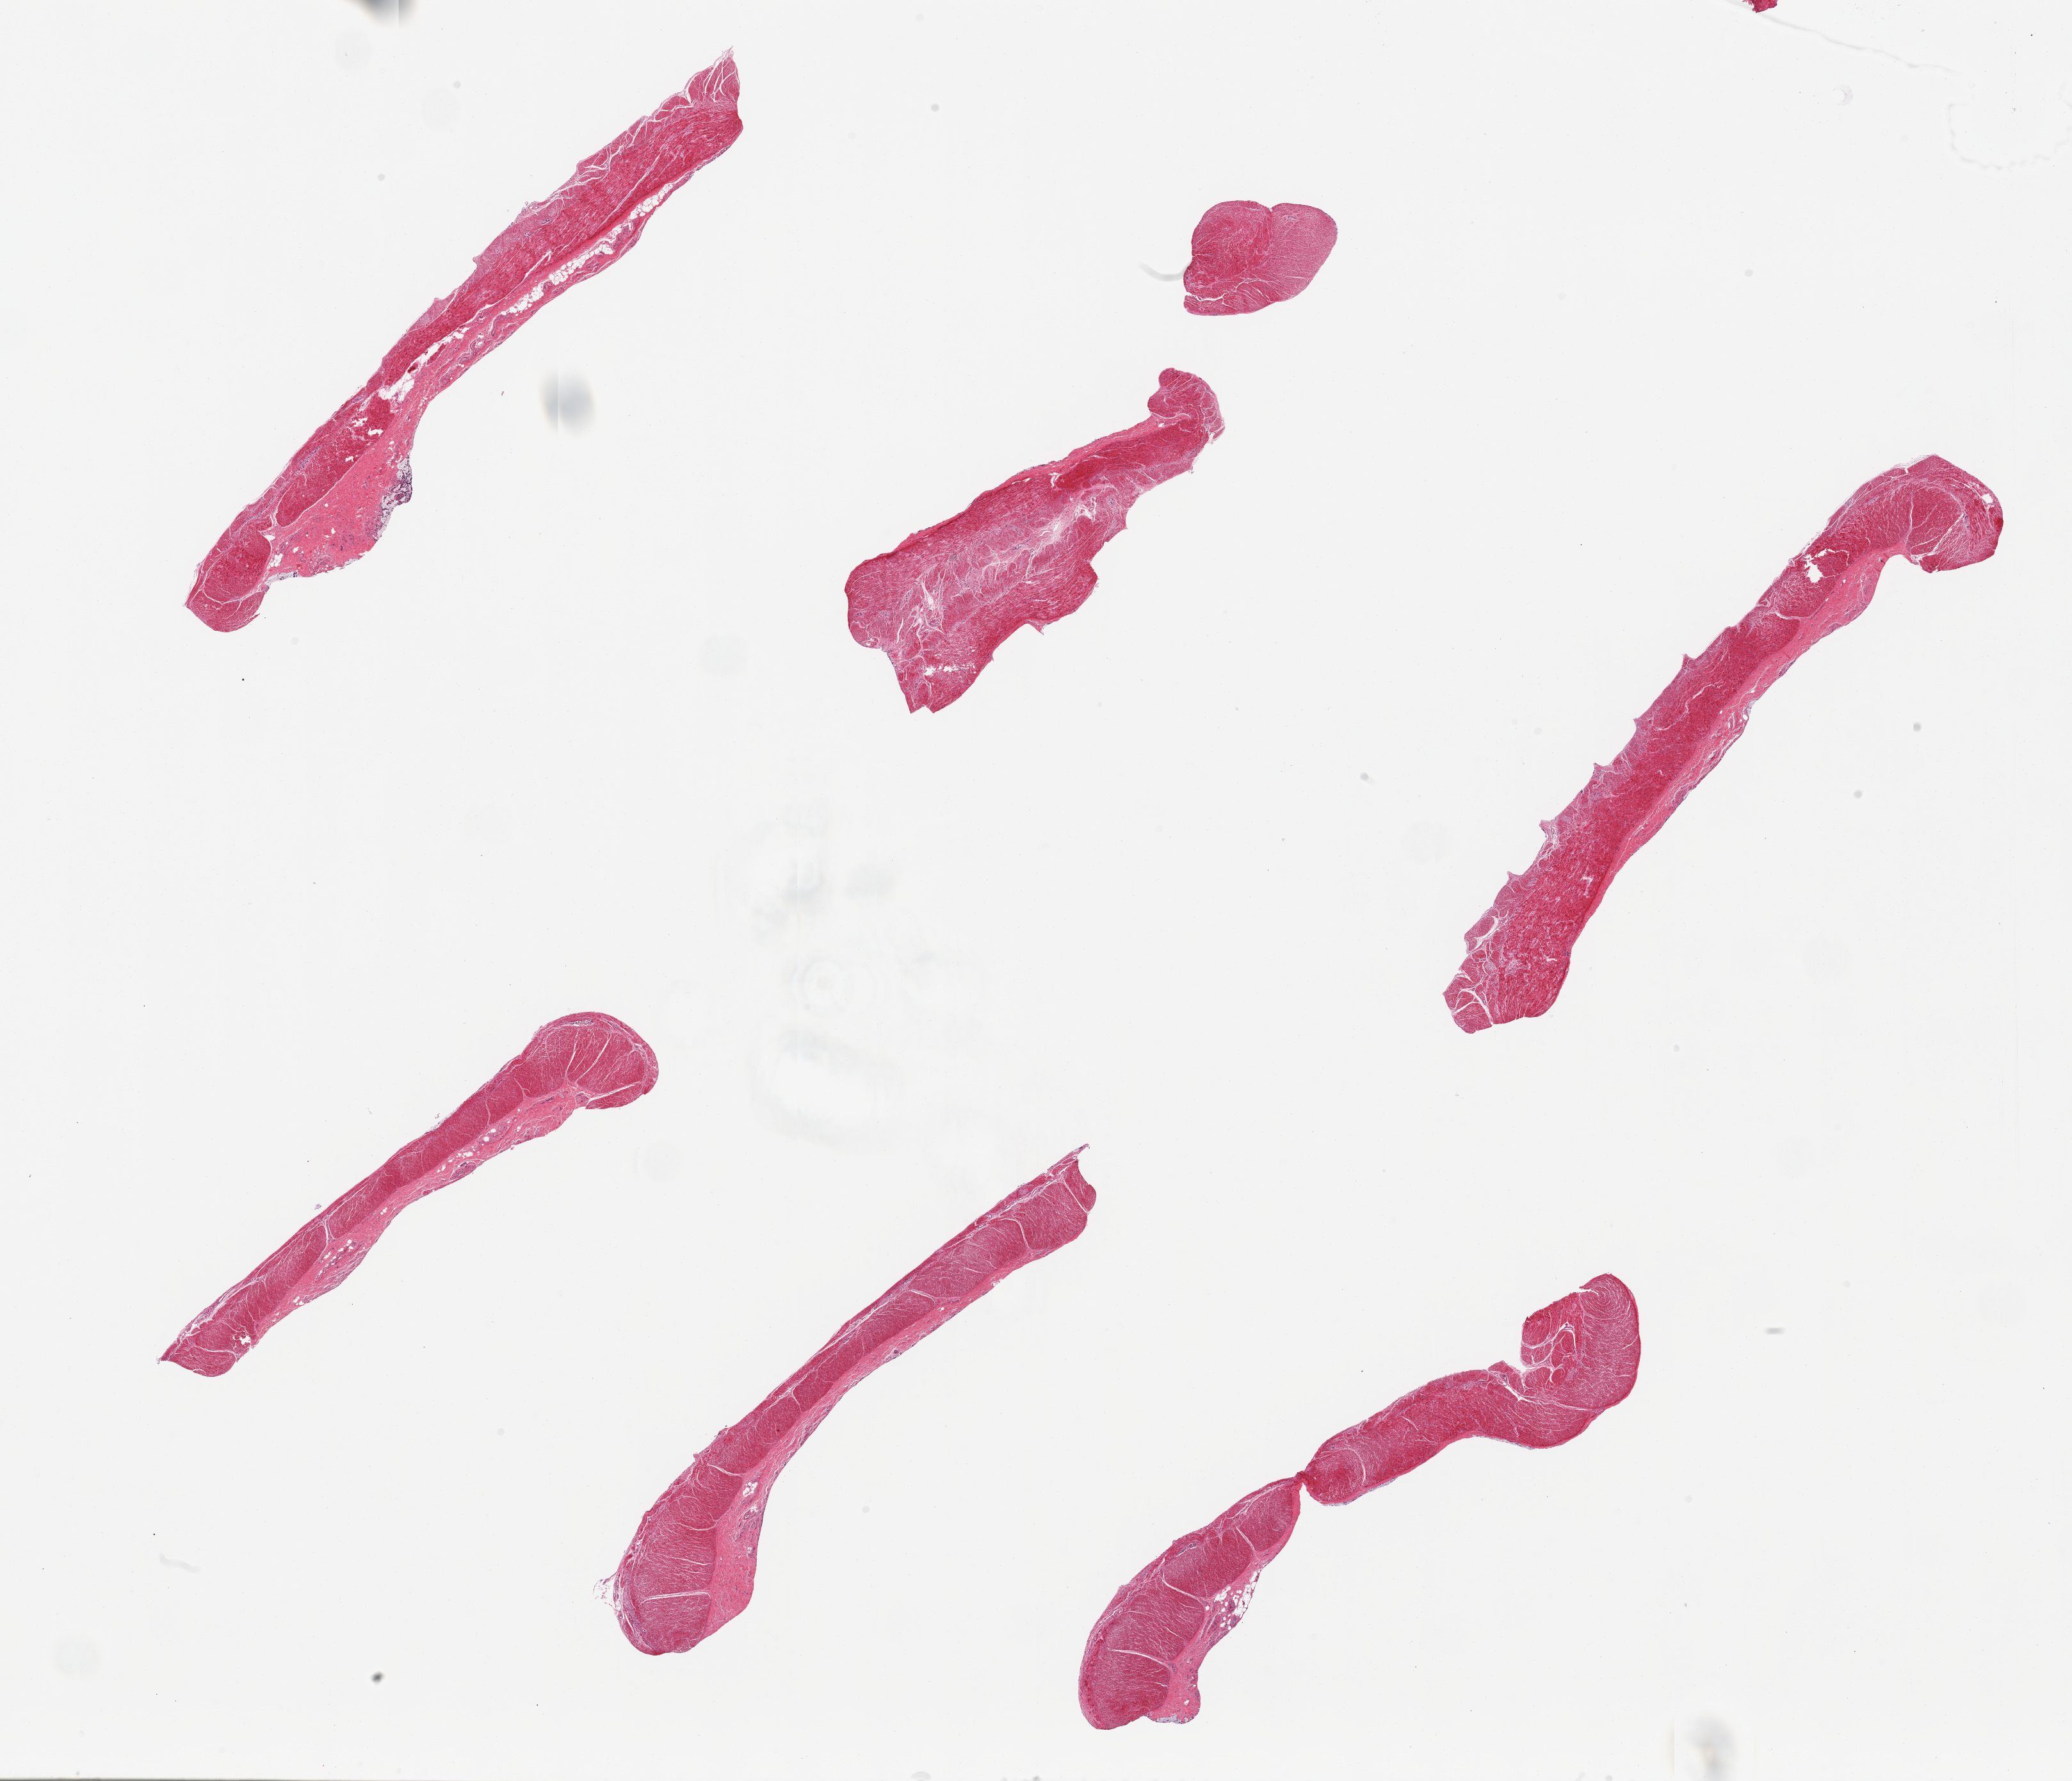
Whole-slide image, hematoxylin and eosin (H&E) stain, brightfield, whole scanned area (about 25.6 x 22.0 mm, slide scanned at 20x) shown as a low-resolution overview, PAXgene-fixed paraffin-embedded (PFPE) section, section of sigmoid colon (target tissue), tissue donor sample. Donor: female.
- pathologist's review note for this sample: 6 pieces, all target muscularis